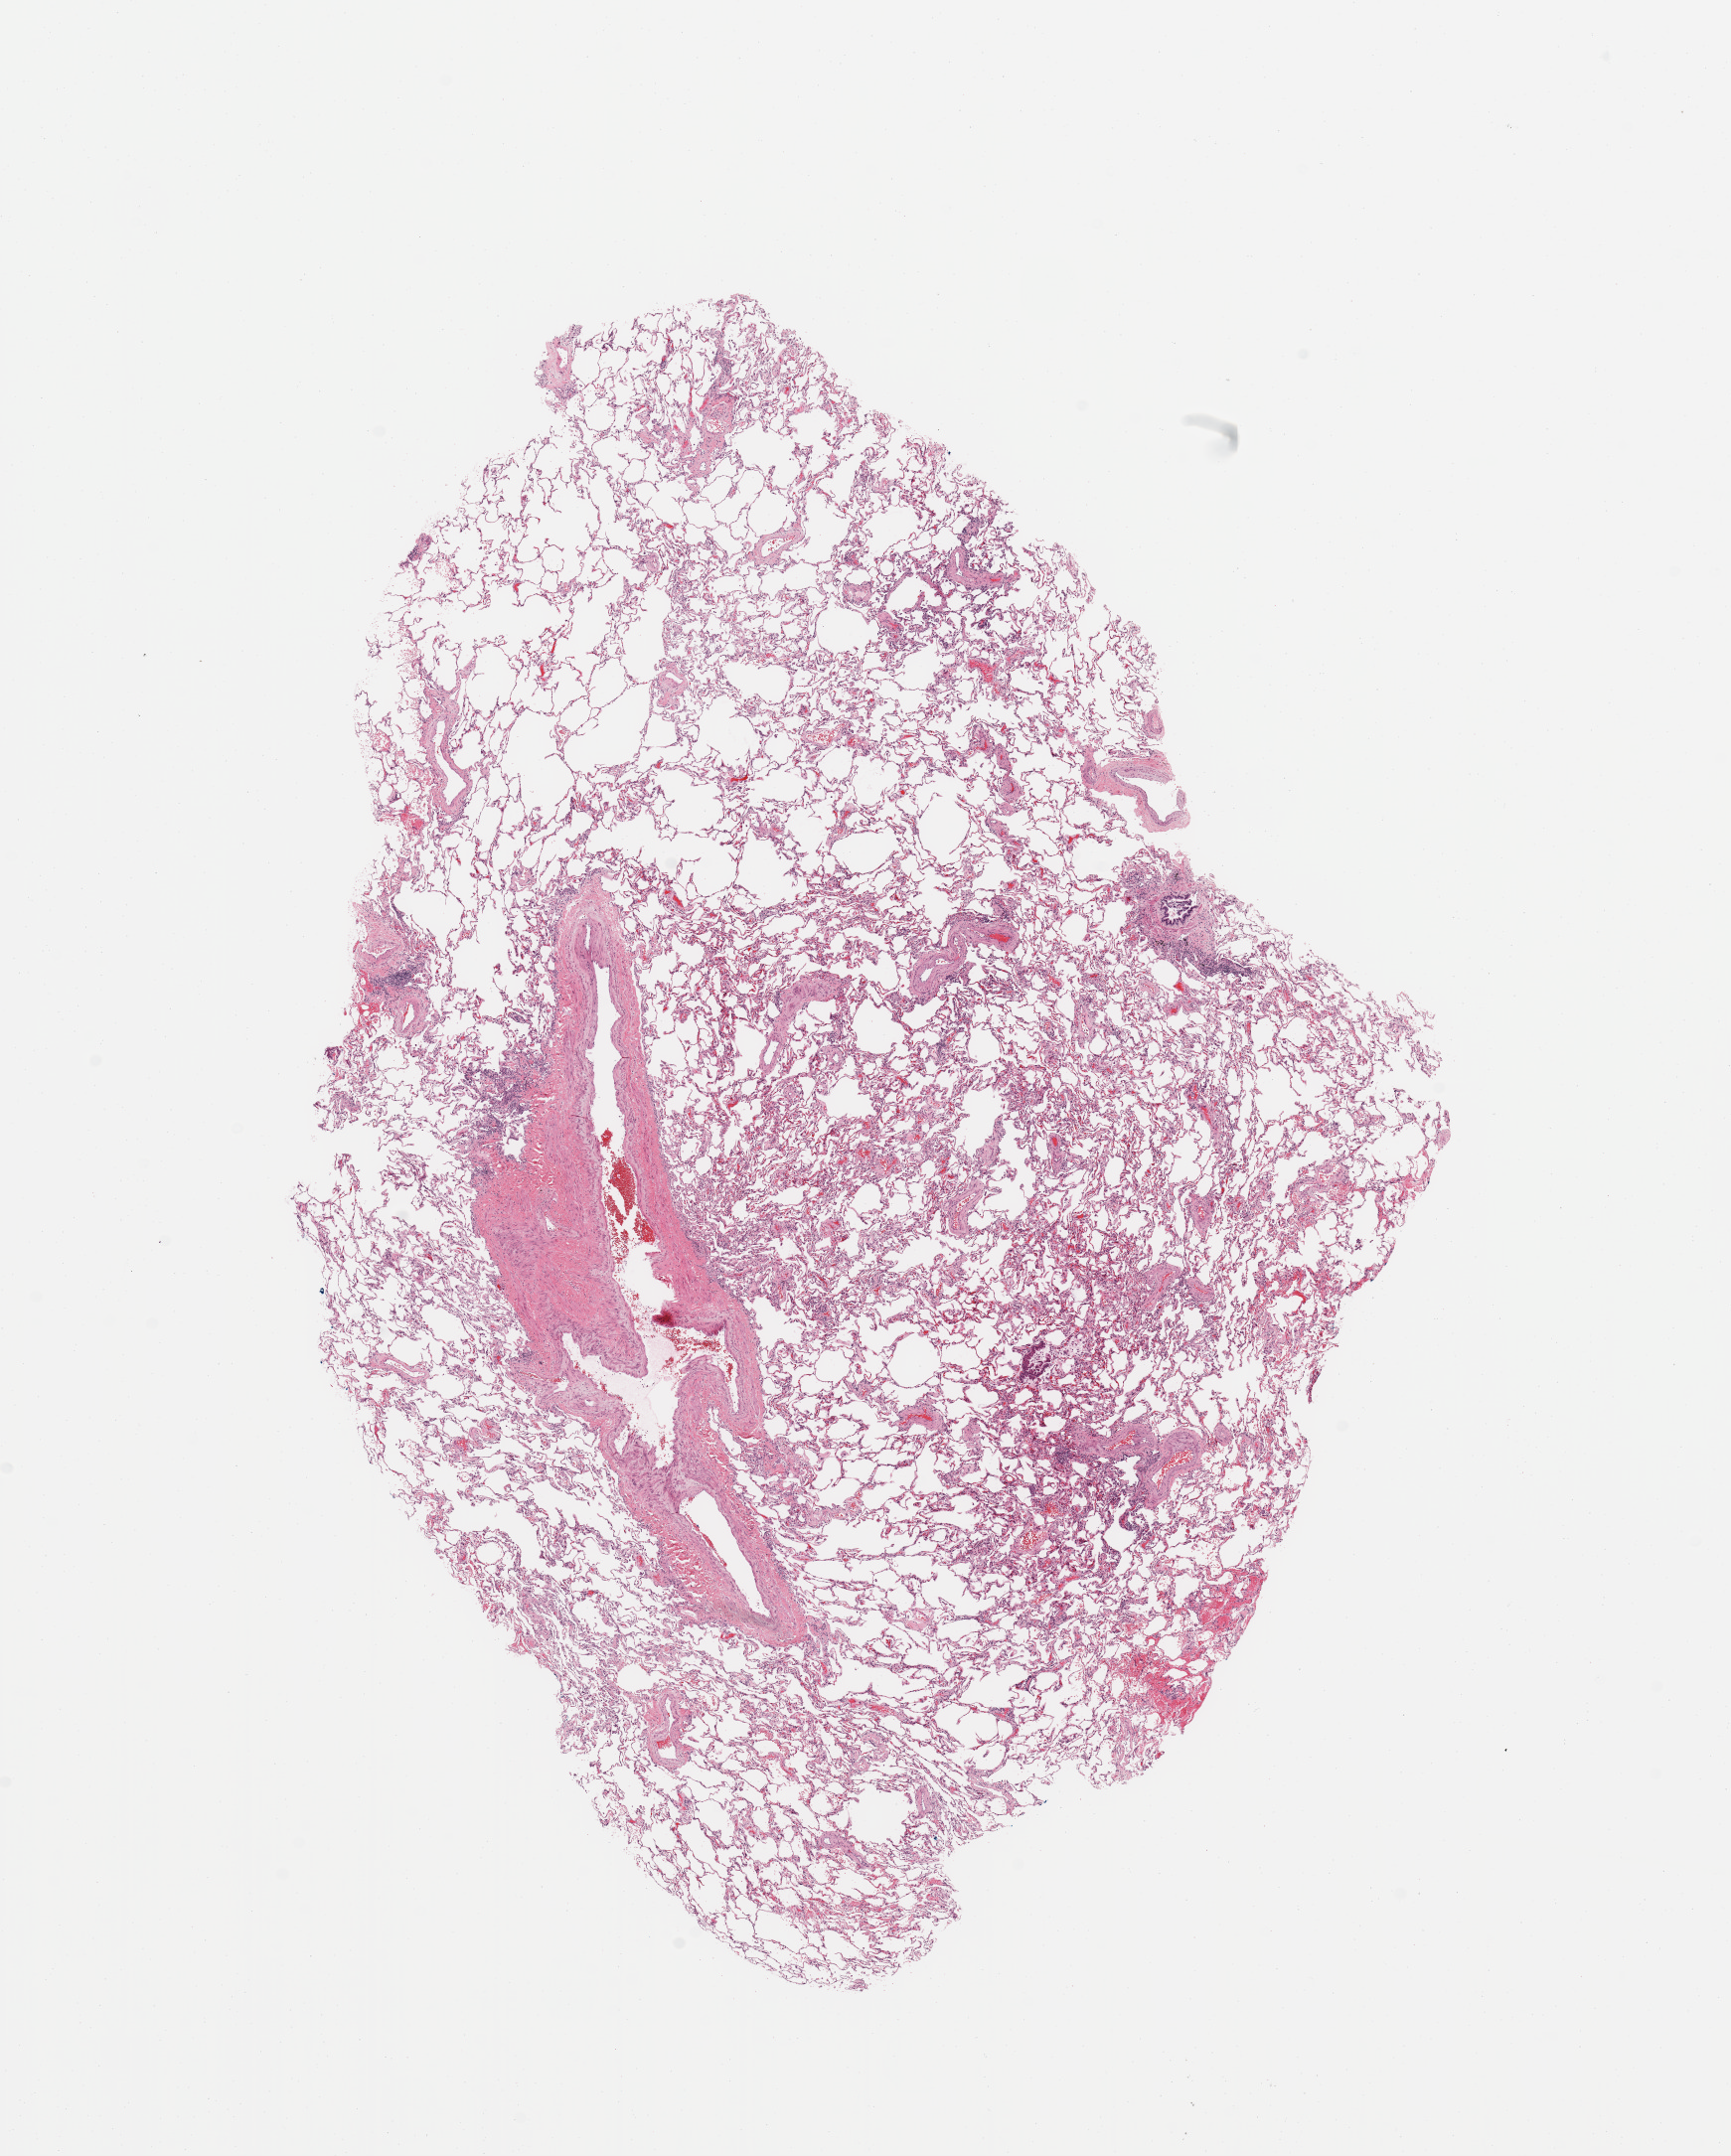
Digitized H&E tissue section (whole slide) — whole scanned area (about 13.8 x 17.2 mm) shown as a low-resolution overview. Normal (non-tumour) tissue sample, sampled site: lung. 69-year-old male patient.
* this section: normal (non-tumour) tissue from the same patient
* patient diagnosis: Adenocarcinoma, NOS